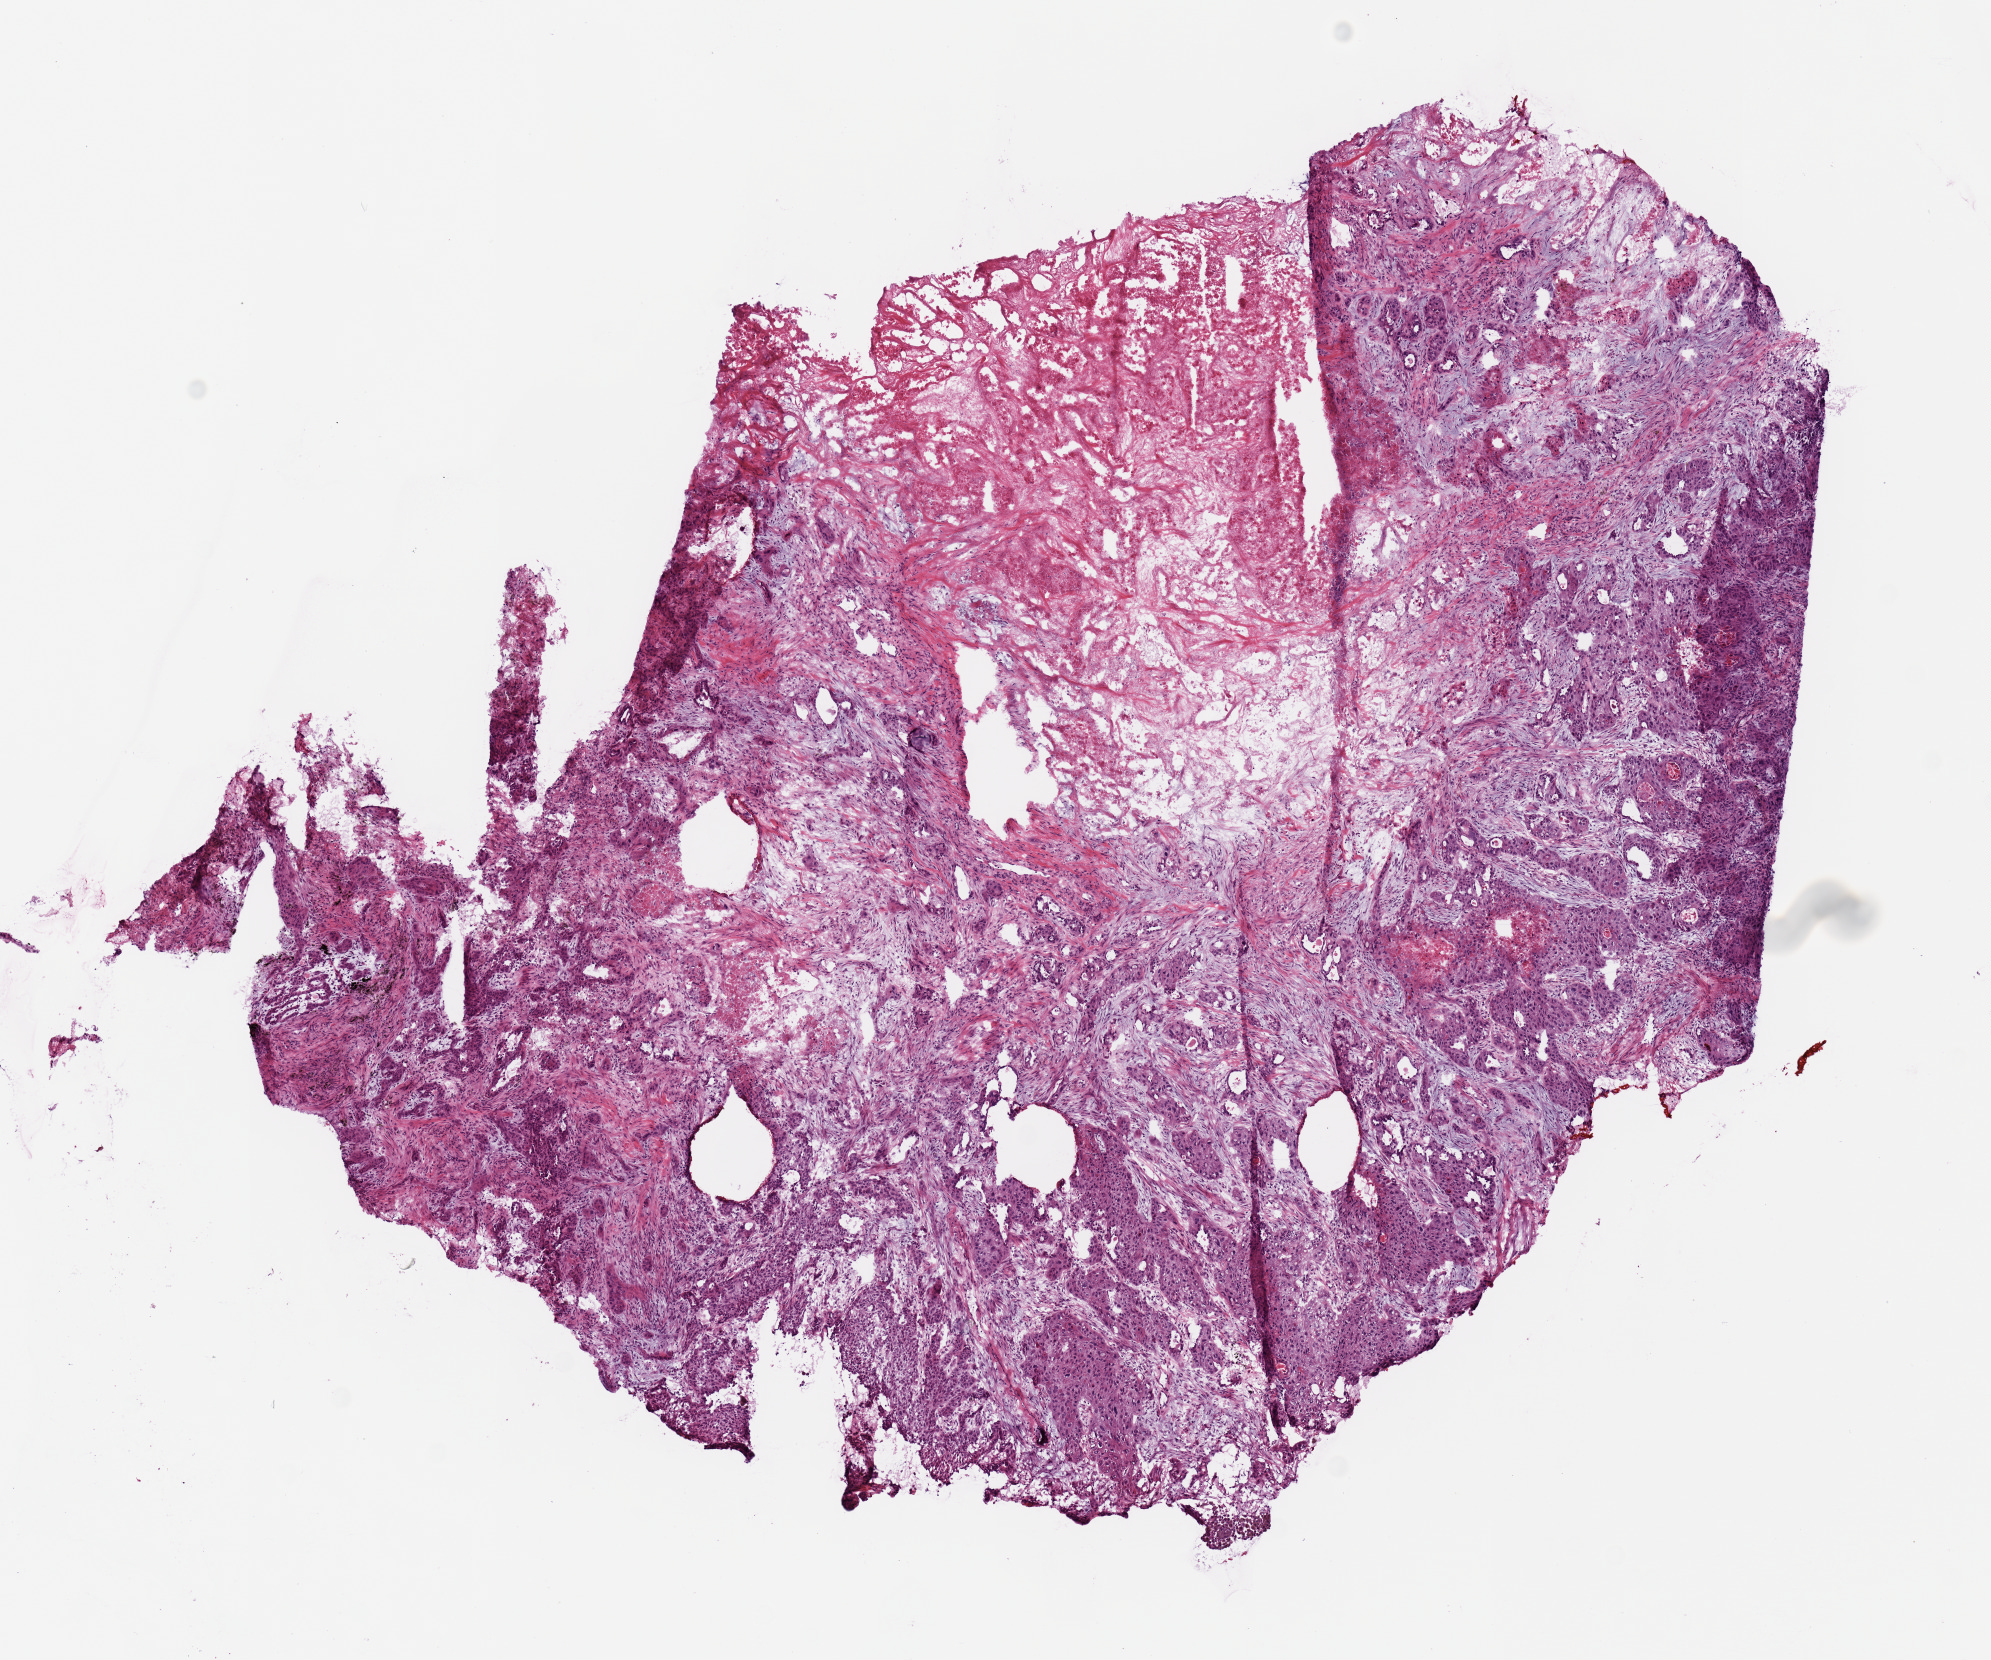
Digitized Hematoxylin and eosin (H&E) stained tissue section (whole slide) — shown as a low-resolution overview of the whole scanned area (about 7.9 x 6.6 mm); frozen section from the top of the tissue portion; primary tumour sample from the lung. Male patient; age at initial diagnosis 59 years. Composition of this section per pathologist review: tumour cells 80%, tumour nuclei 60%, normal cells 0%, stromal cells 20%, necrosis 0%.
AJCC pathologic stage: IA (7th edition). Laterality: left. Diagnosis: Squamous cell carcinoma, NOS.